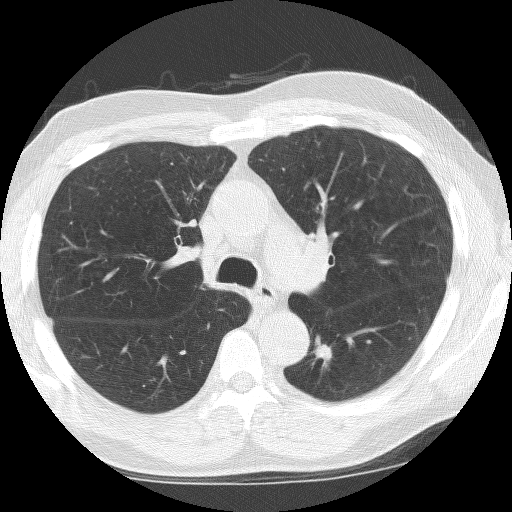
Low-dose screening chest CT, one axial slice. Slice 98 of 155 in the series (ordered by position). Reconstruction kernel BONE. 120 kVp. Lung window (W 1500 / L -600 HU). 2.5 mm slice thickness. 512 × 512 image matrix.
Annotated regions visible in this slice (manually delineated by an expert):
- lesion 1 (tumor, lower lobe of left lung): box from (x=313, y=336) to (x=332, y=369) px